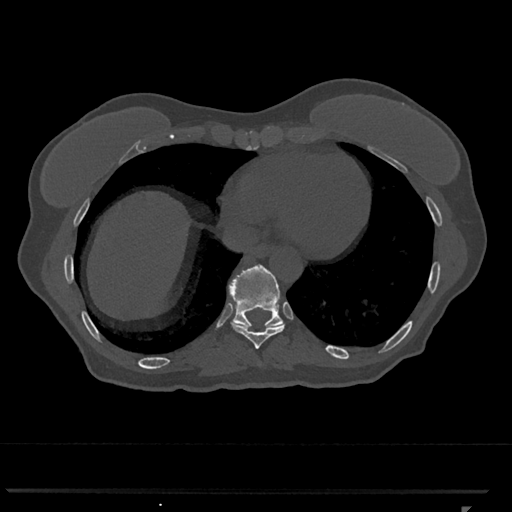
CT including the spine, one axial slice. 120 kVp. Bone window (W 1800 / L 400 HU). 0.5 mm slice thickness. 512 × 512 image matrix, field of view 380 × 380 mm. Female patient, age 62 years. Case-level facts recorded for this patient, not image findings: primary cancer: renal.
Structures marked on this image (semi-automatically segmented with operator editing):
- T10 vertebra: bounding box <229,265,283,328> (left, top, right, bottom; pixels)
- T9 vertebra: <231,307,285,349>